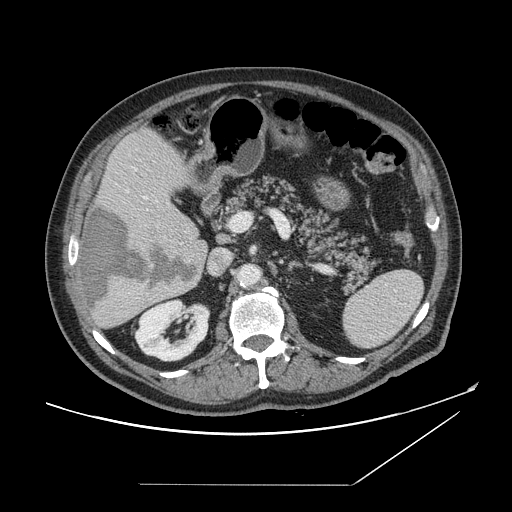
Contrast-enhanced abdominal CT, one axial slice. Position 83 of 166 along the scan axis. 120 kVp. Intravenous contrast given. Soft-tissue window (W 400 / L 40 HU). 512 × 512 image matrix, field of view 416 × 416 mm. Male patient, age 80 years. From the clinical record (not read from this slice): diagnosis: colorectal cancer liver metastases, imaged before liver resection; multiple liver metastases: no; largest metastasis: 2.2 cm; disease in both lobes: no.
Structures marked on this image (expert manual segmentation):
- hepatic veins: bounding box (x1, y1, x2, y2) in pixels: (145, 197, 148, 200)
- liver: (78, 129, 208, 329)
- planned liver remnant (the part of the liver to remain after resection): (101, 129, 200, 237)
- portal vein (with intrahepatic branches): (229, 224, 231, 227)
- liver metastasis: (82, 206, 196, 309)